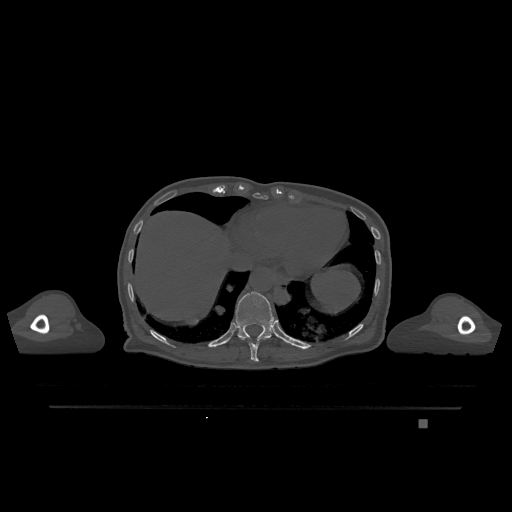
CT including the spine, one axial slice; bone window (W 1800 / L 400 HU); 0.5 mm slice thickness; 512 × 512 image matrix, field of view 500 × 500 mm. Patient: female, 74 years. Case-level facts recorded for this patient, not image findings: primary cancer: lung; vertebrae with lytic lesions (as recorded): T1, T4, T5, T6, L4, L5.
Outlined on this slice (semi-automatically segmented with operator editing):
- T10 vertebra: bounding box [x1, y1, x2, y2] px = [239, 337, 268, 362]
- T11 vertebra: [228, 291, 276, 341]